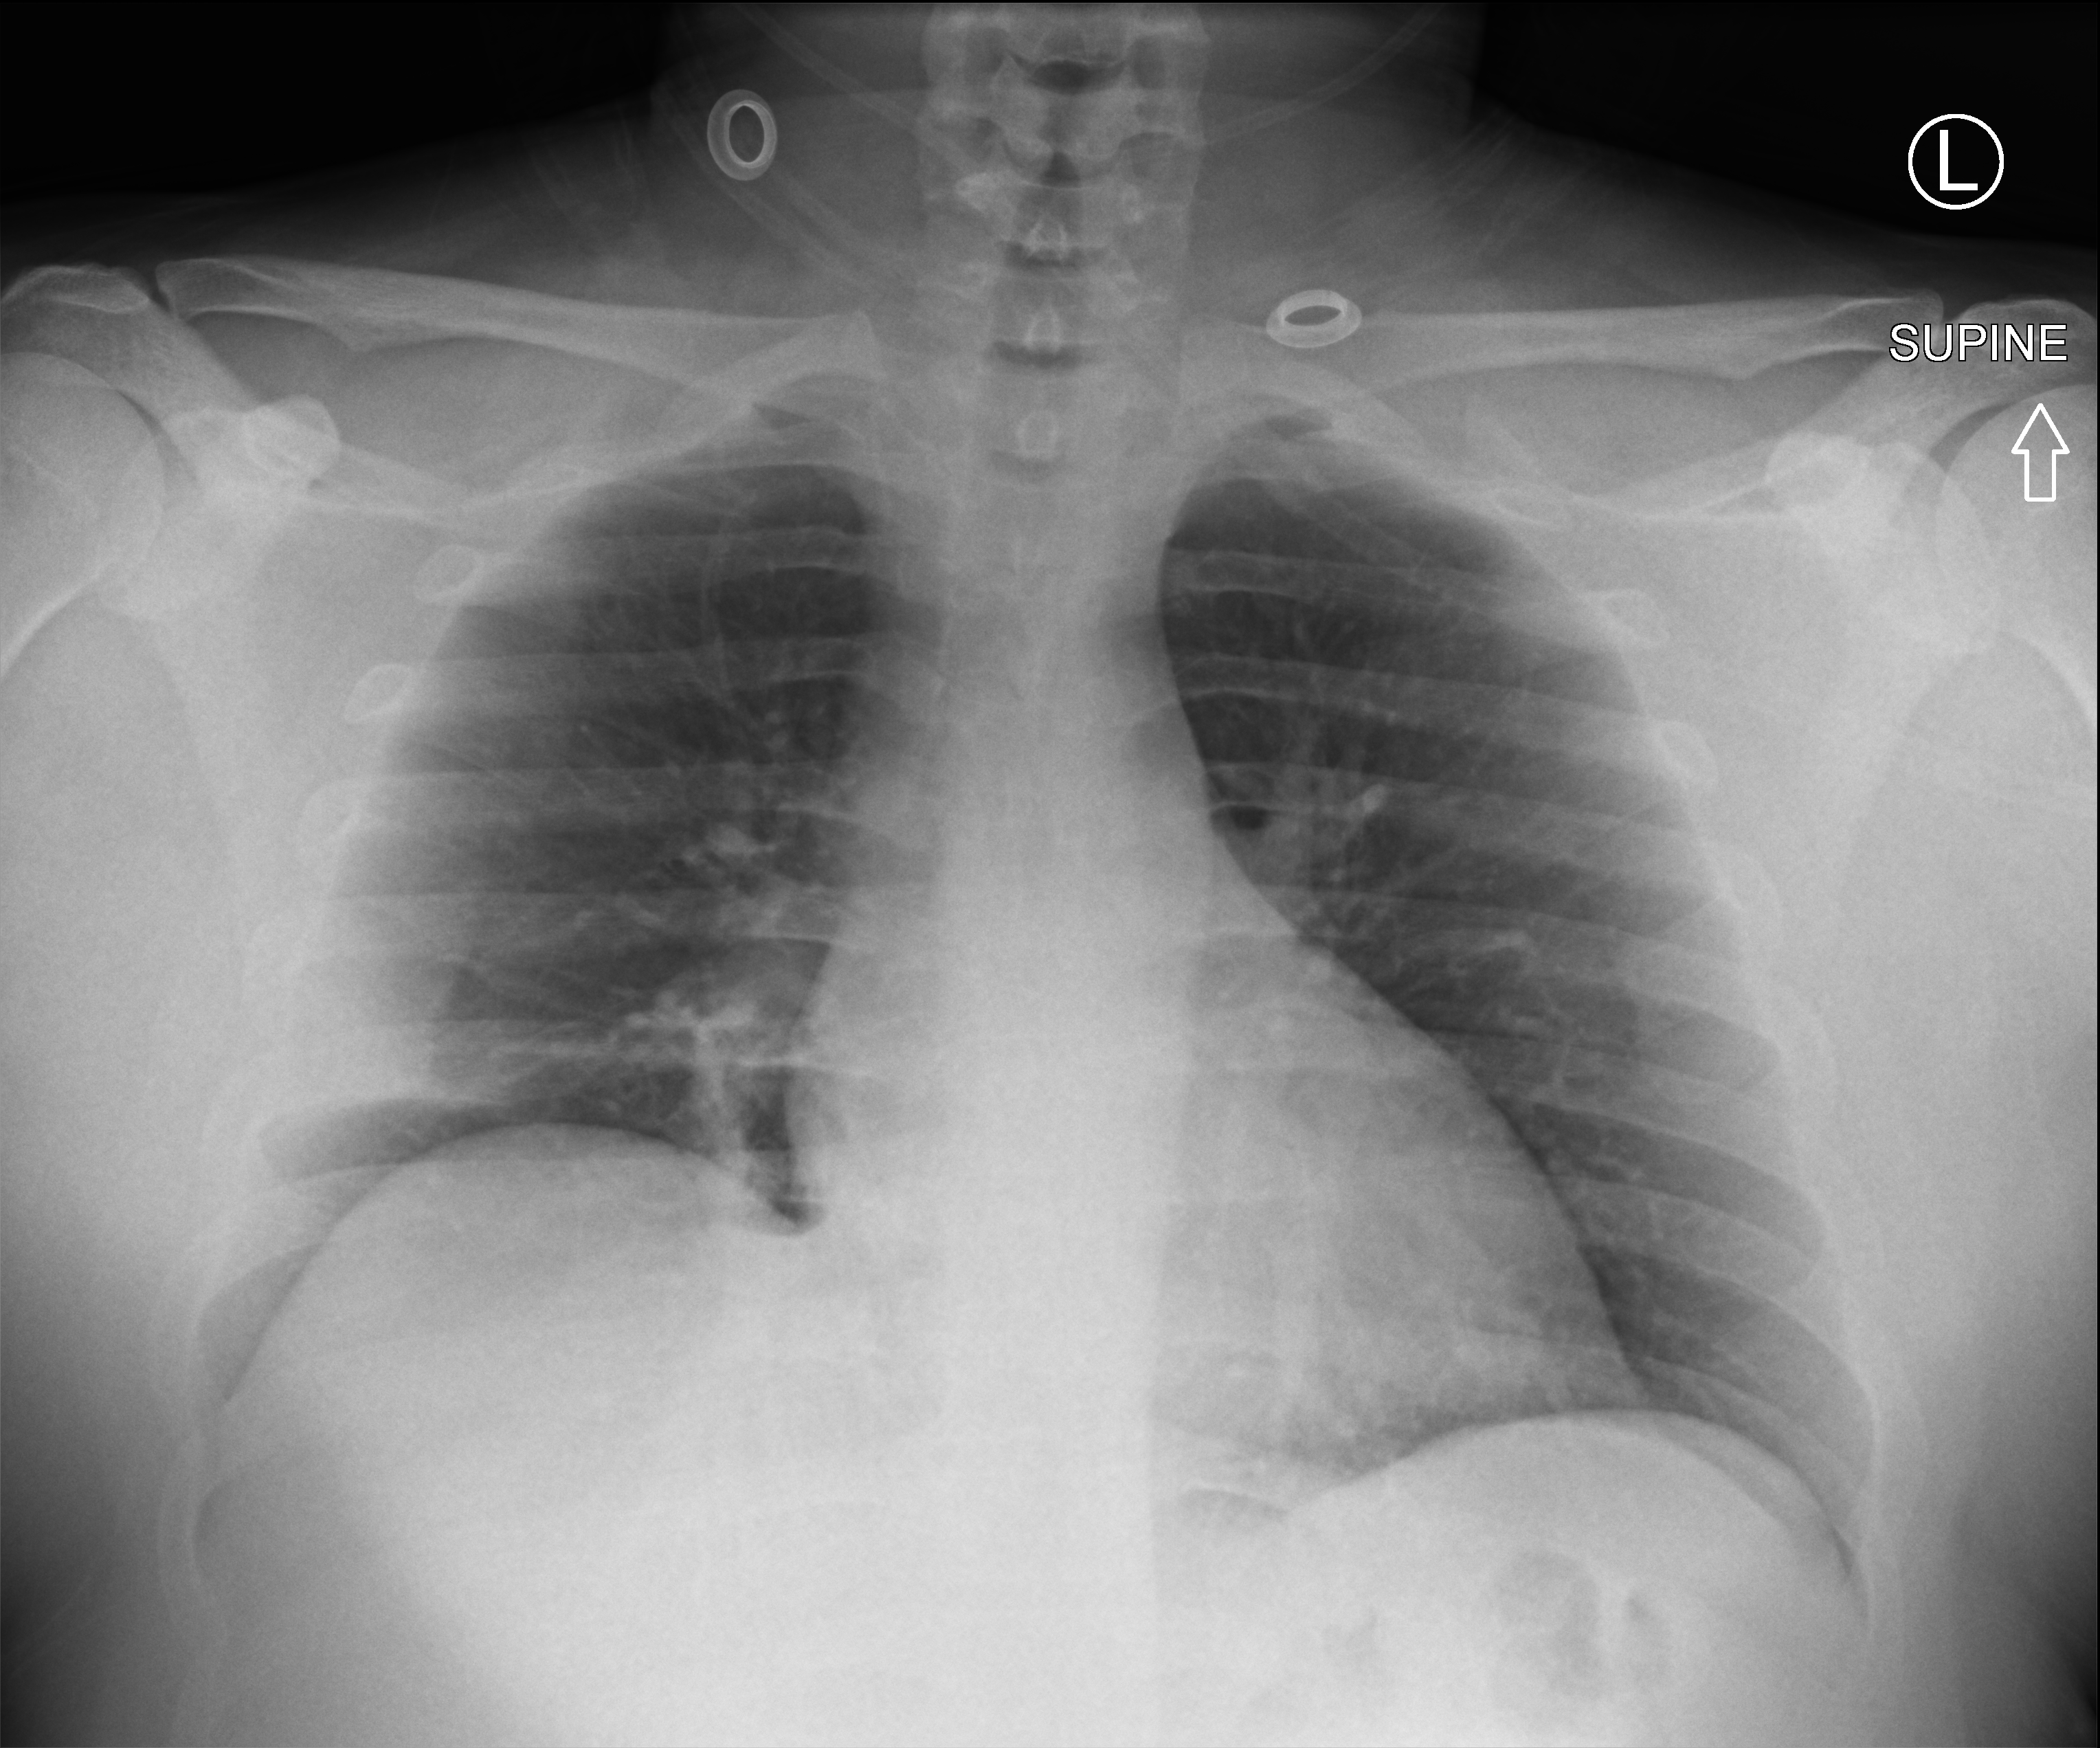
Portable chest radiograph, anteroposterior (AP) projection. Patient hospitalised with COVID-19; male, aged 18–59 years.
Hospital-stay facts (about this admission, not read from this image; timing relative to this image not recorded): mechanically ventilated during this hospital stay: no; length of hospital stay: 4 days.